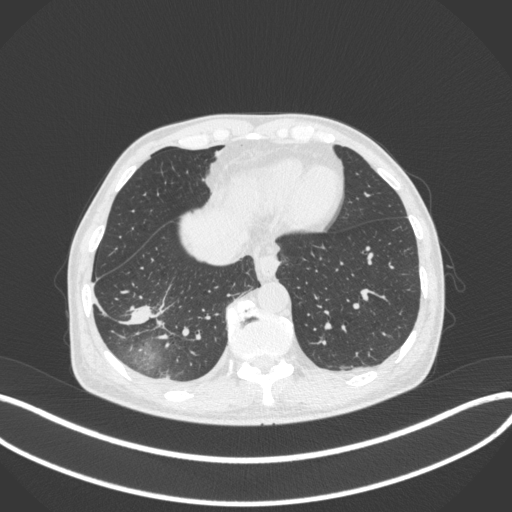
Chest CT, one axial slice; slice 94 of 385 in the series (ordered by position); 120 kVp; lung window (W 1500 / L -600 HU); 512 × 512 image matrix, field of view 400 × 400 mm. Patient: male, 64 years. Case-level facts recorded for this patient, not image findings: clinical TNM (as recorded): T3 N0 M0; histopathological grade: G2-3.
Outlined on this slice (rectangle marked by the reading radiologist):
- lung tumour (recorded histology: adenocarcinoma): bounding box <123,297,155,332> (left, top, right, bottom; pixels)